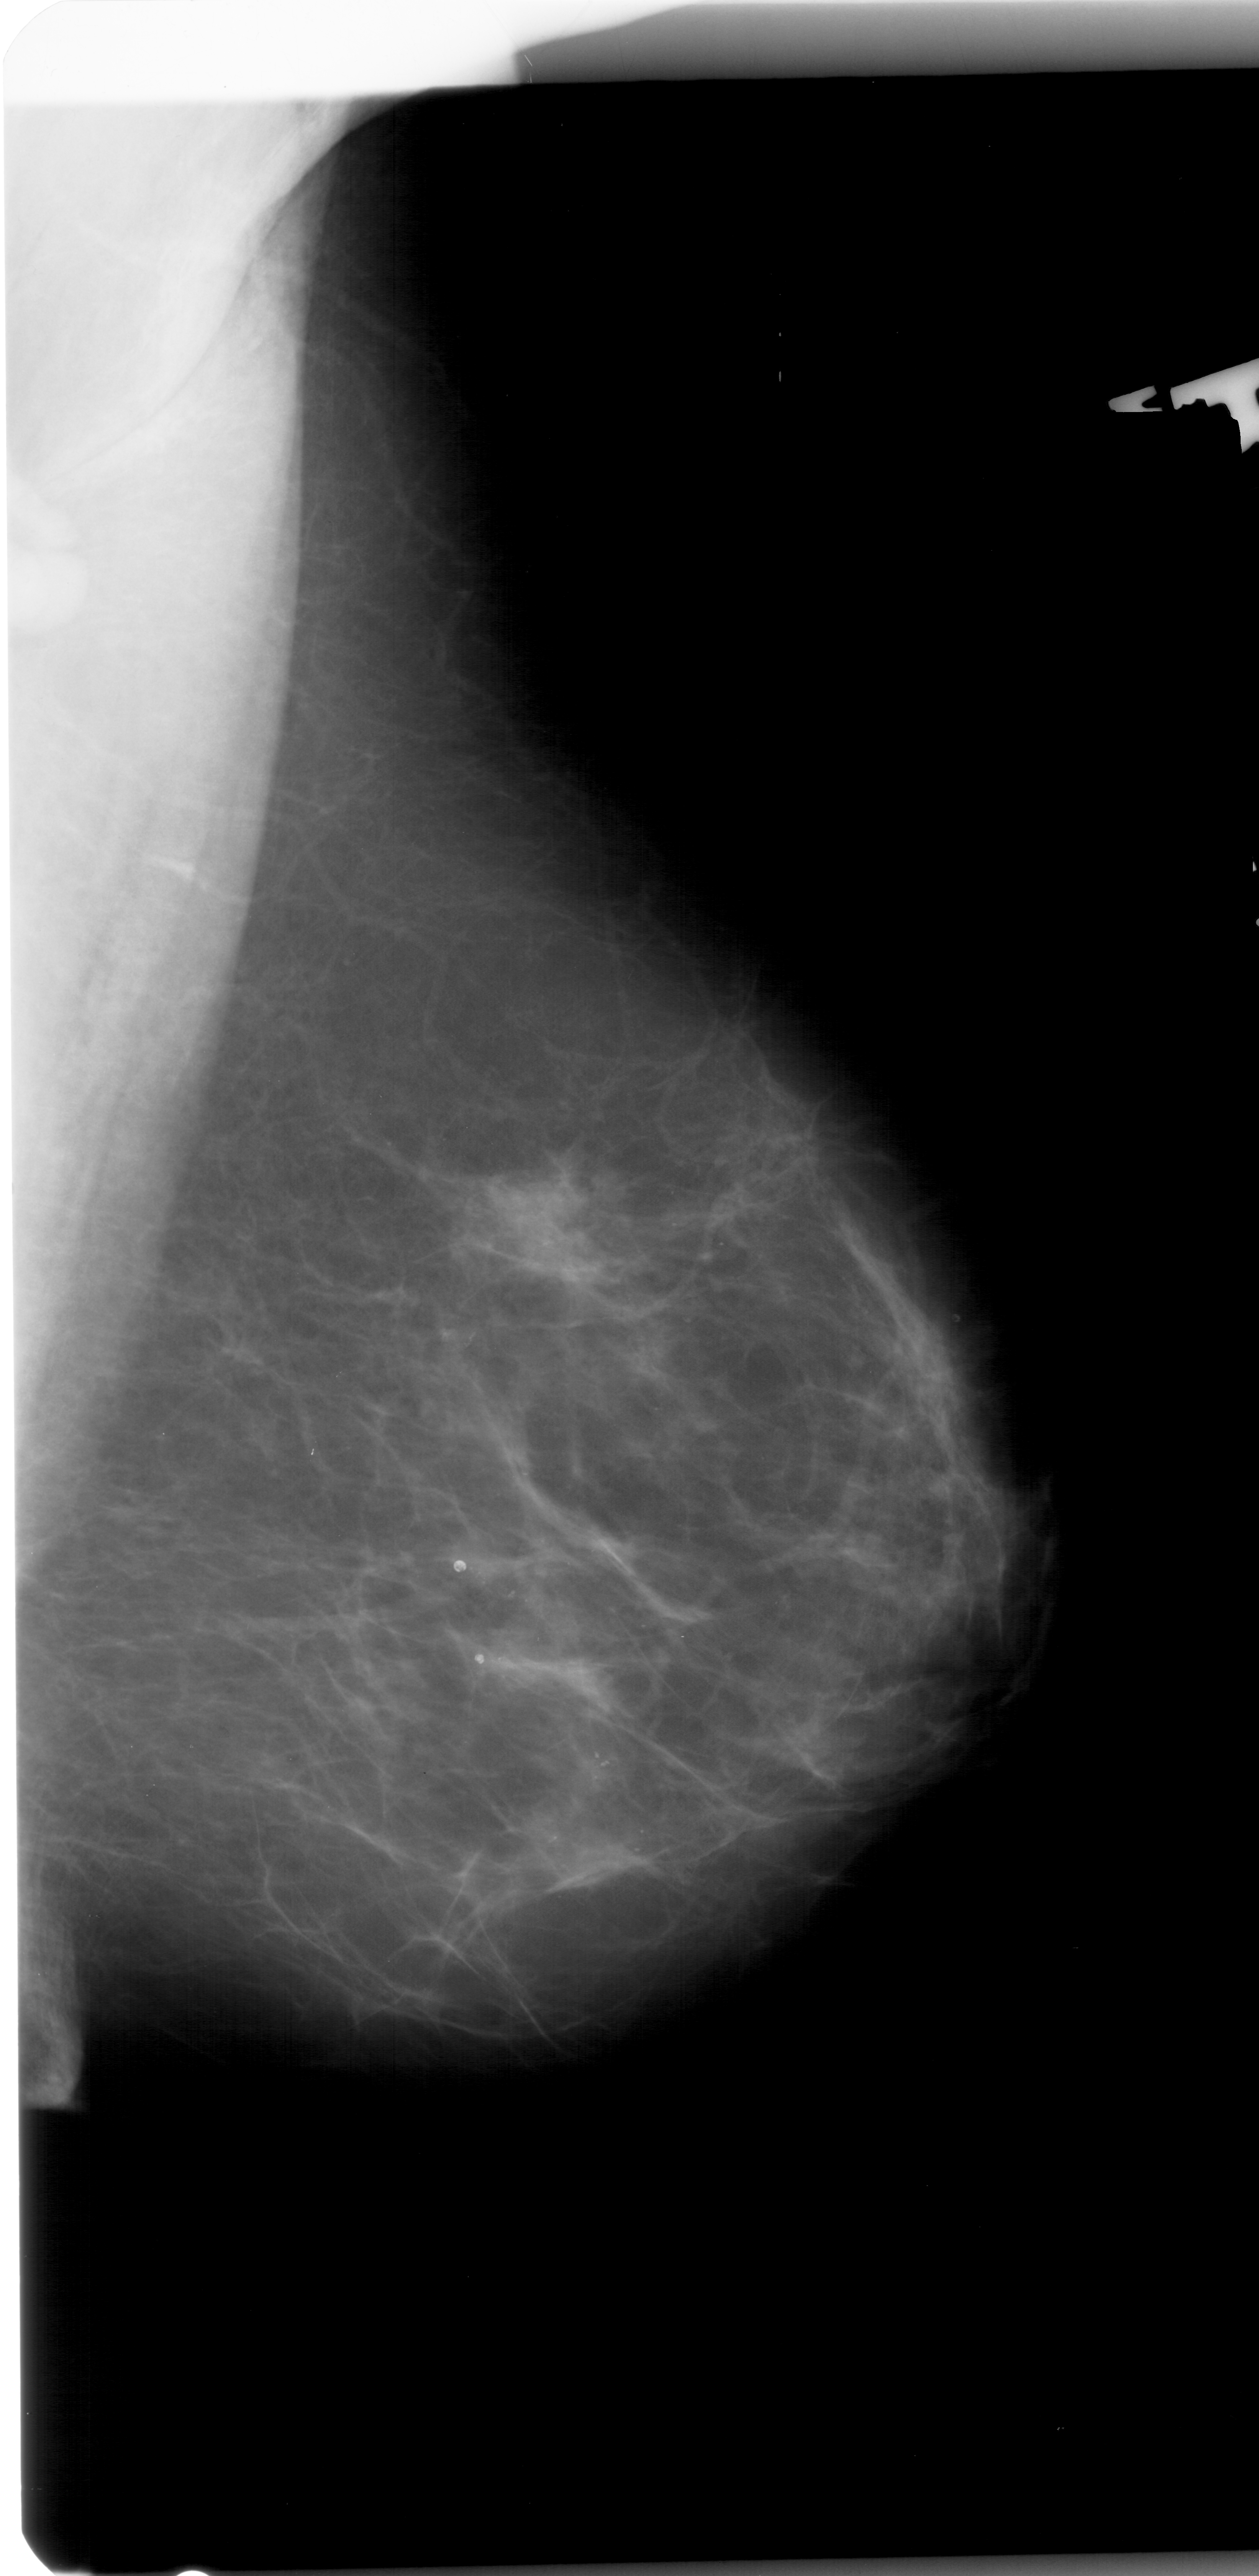
Scanned film-screen mammogram; right breast; mediolateral oblique (MLO) view.
Radiologist-marked abnormalities on this image: calcifications, morphology pleomorphic, distribution clustered; BI-RADS assessment category 4; subtlety rating 2 on a 1 (subtle) to 5 (obvious) scale; pathology (as recorded): benign.